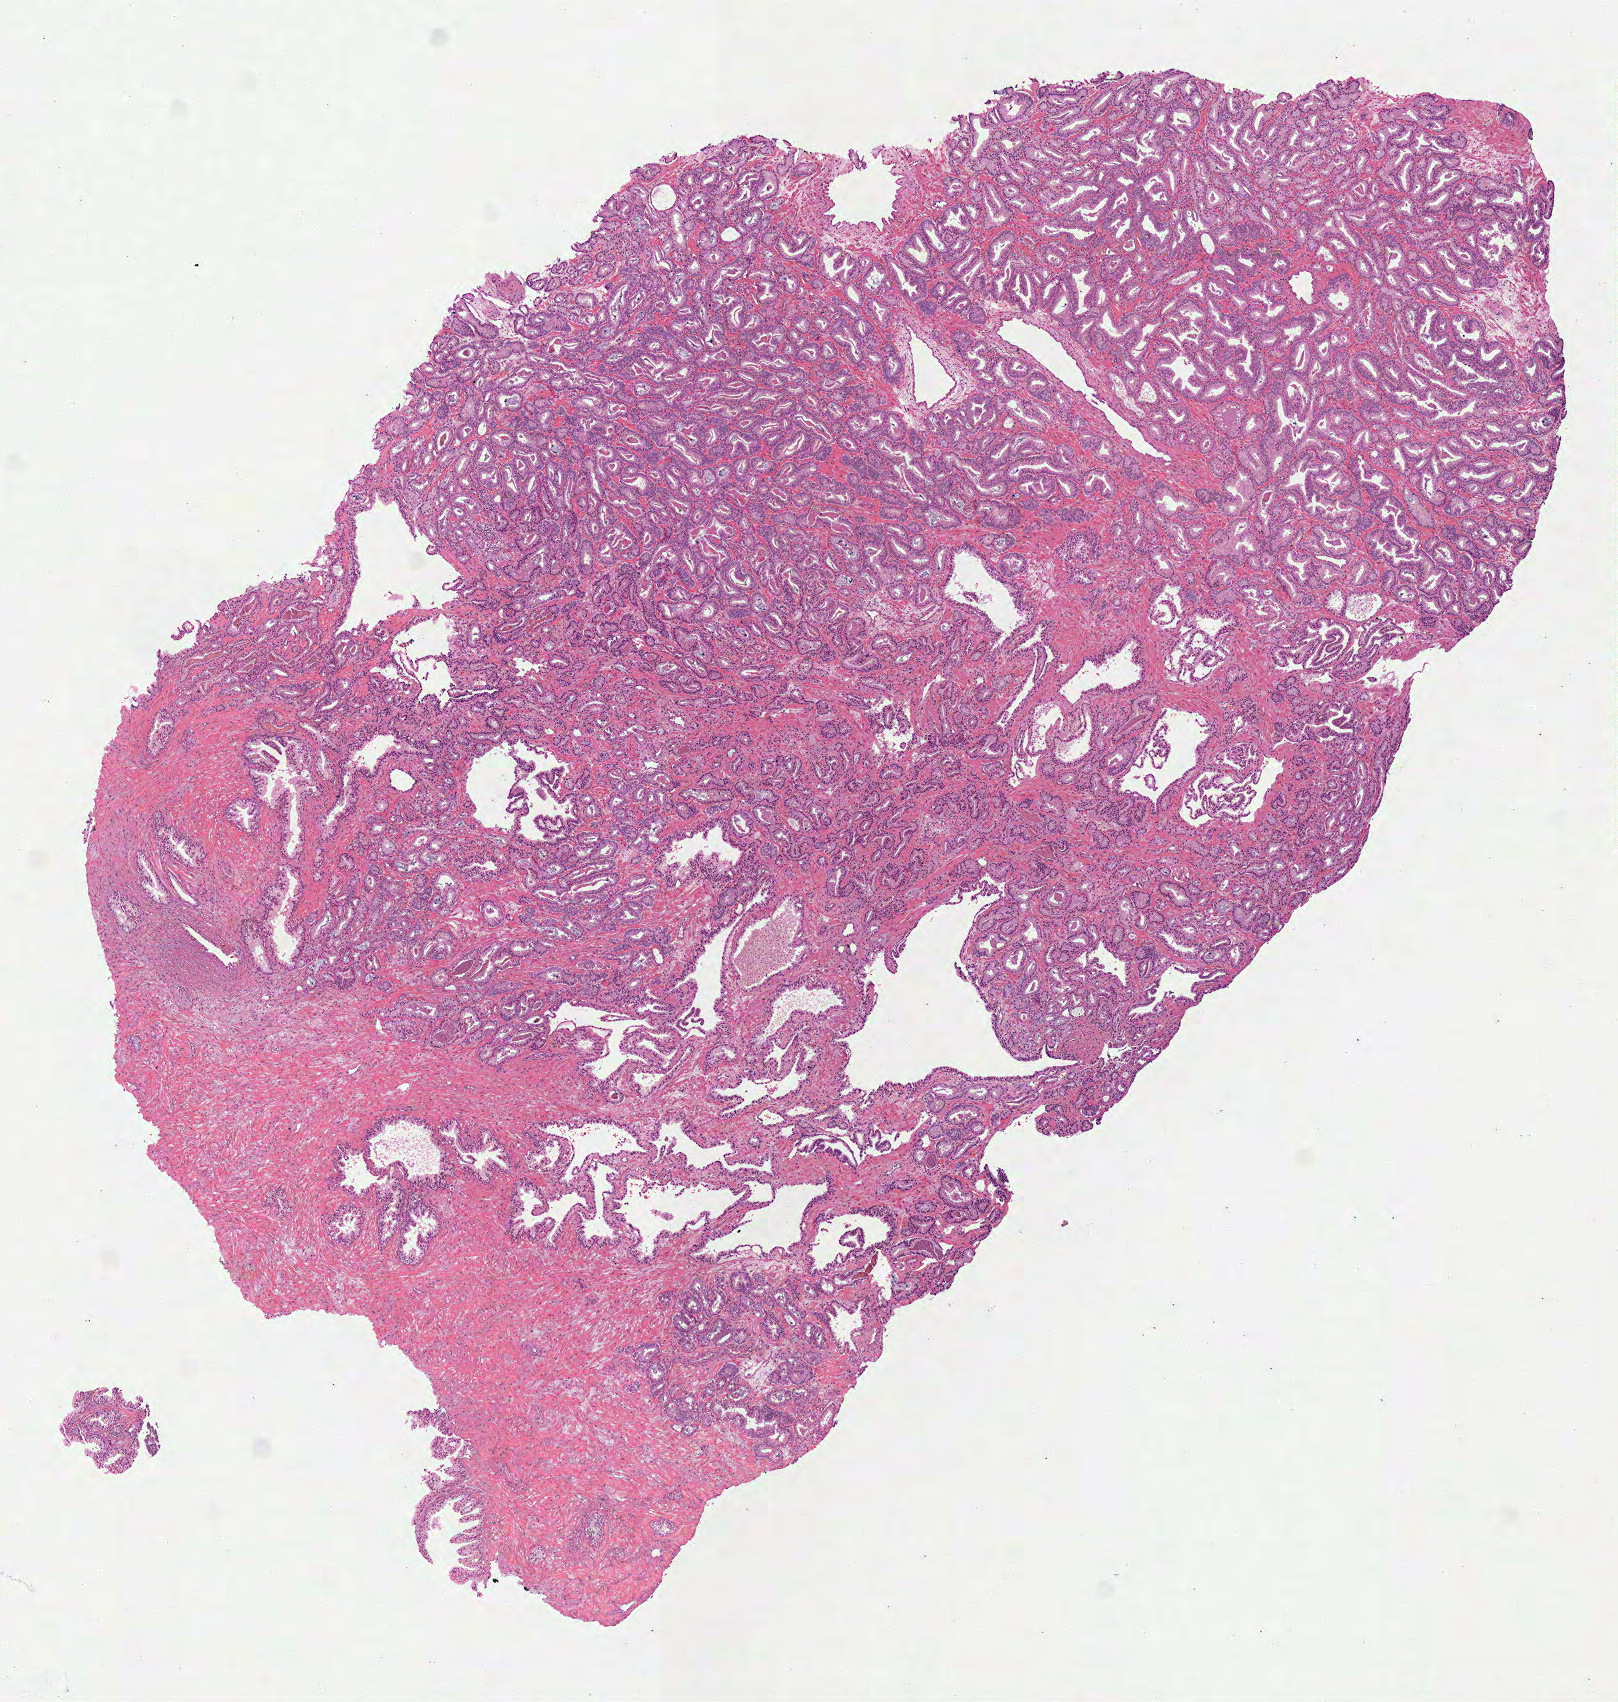
Digitized H&E tissue section (whole slide), a low-resolution overview of the entire scanned area, about 6.5 x 6.9 mm. Formalin-fixed paraffin-embedded (FFPE) diagnostic section. Sample: primary tumour, prostate. Patient: male, age at initial diagnosis 50 years. Gleason score: 6 (3+3).
- histologic diagnosis: Acinar cell carcinoma (prostate gland)